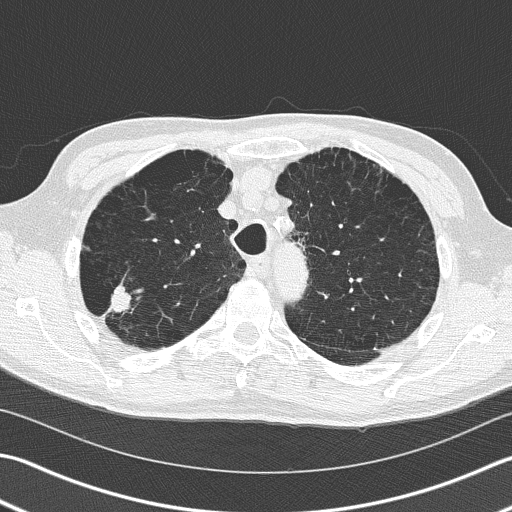
Chest CT (low-dose screening protocol), one axial image; first (baseline) screen; lung window (W 1500 / L -600 HU); 2 mm slice thickness; lung (sharp) reconstruction kernel (B50f); 120 kVp; slice 42 of 163 in the series. Male, age 66 years at enrolment. Current smoker at enrolment.
• Expert reader's lesion annotation, box from (x=82, y=265) to (x=144, y=339) px.
• Reader record for this screening exam (exam-level; its link to the box is not recorded): non-calcified nodule or mass ≥4 mm, right upper lobe, 39 × 23 mm, spiculated (stellate) margins, soft tissue attenuation.
• Official screen result: positive, change unspecified: nodule(s) >= 4 mm or enlarging nodule(s), mass(es), or other non-specific abnormalities suspicious for lung cancer.
• Later outcome: lung cancer diagnosed 36 days after this screen — squamous cell carcinoma, NOS, right upper lobe, poorly differentiated (G3), stage IB (AJCC 6th edition), 23 mm at pathology.